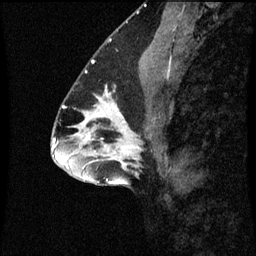
Breast MRI (dynamic contrast-enhanced), one sagittal slice. Dynamic contrast-enhanced series, image 2 of 3 at this slice position (ordered by acquisition). 1.5 T. TE 4.2 ms, TR 8.9 ms. 2 mm slice thickness. 256 × 256 image matrix. Female patient, age 43 years. From the clinical record (not read from this slice): setting: breast cancer imaged before/during neoadjuvant chemotherapy; receptor status: HR-positive, HER2-negative.
Annotated regions visible in this slice (semi-automatically segmented with operator editing):
- analysis volume of interest (the breast-tissue region the enhancement analysis was run in; not a lesion): bounding box <96,96,159,159> (left, top, right, bottom; pixels)
- tumour enhancement mask (voxels above the 70 % enhancement threshold inside the analysis volume of interest): <106,96,109,149>